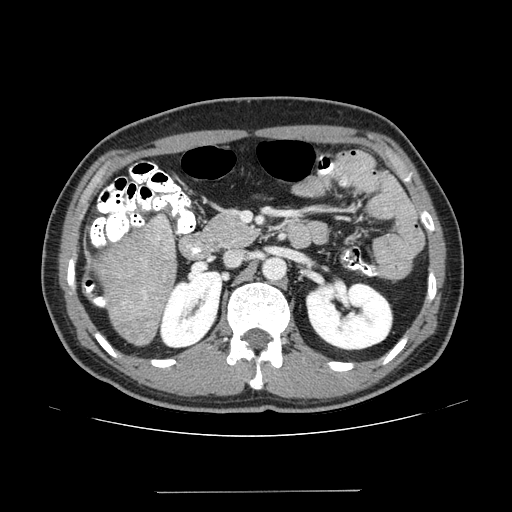
Contrast-enhanced abdominal CT (liver protocol), one axial slice. Slice 63 of 131 in the series (ordered by position). 100 kVp. One of 2 acquisitions stored at this slice position. Soft-tissue window (W 400 / L 40 HU). 2.5 mm slice thickness. 512 × 512 image matrix, field of view 380 × 380 mm. Case-level facts recorded for this patient, not image findings: diagnosis: hepatocellular carcinoma (patient treated with transarterial chemoembolisation; whether this scan precedes or follows treatment is not stated here); TNM stage (as recorded): Stage-I; Child-Pugh class: A.
Annotated regions visible in this slice (semi-automatically segmented with operator editing):
- liver parenchyma outside the tumour (the mass and vessels are separate outlines, so this box may not span the whole liver): bounding box (x1, y1, x2, y2) in pixels: (84, 250, 168, 343)
- mass: (100, 249, 145, 278)